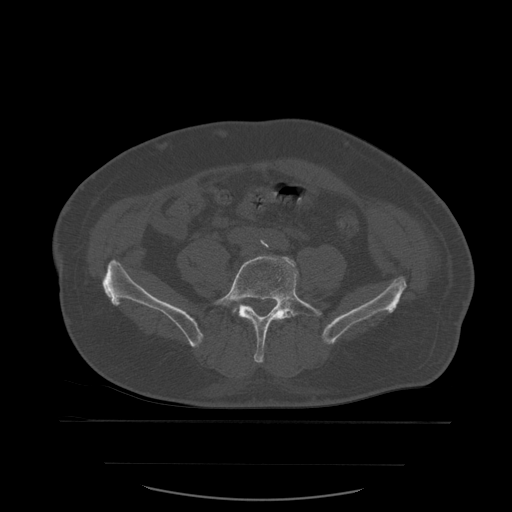
CT including the spine, one axial slice; slice 140 of 590 in the series (ordered by position); bone window (W 1800 / L 400 HU); 1.25 mm slice thickness; 512 × 512 image matrix. Patient age 71 years. Case-level facts recorded for this patient, not image findings: primary cancer: lung.
Annotated regions visible in this slice (semi-automatically segmented with operator editing):
- L5 vertebra: bounding box [x1, y1, x2, y2] px = [213, 255, 322, 364]